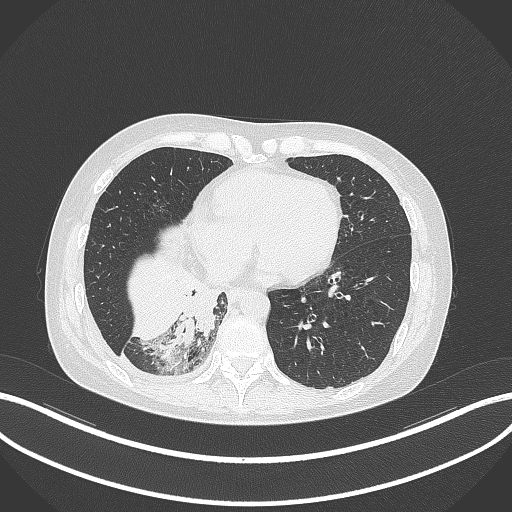
Chest CT, one axial slice; slice 97 of 329 in the series (ordered by position); 120 kVp; lung window (W 1500 / L -600 HU); 1 mm slice thickness; 512 × 512 image matrix, field of view 400 × 400 mm. Female patient, age 63 years. Case-level facts recorded for this patient, not image findings: clinical TNM (as recorded): T1c N0 M0.
Annotated regions visible in this slice (rectangle marked by the reading radiologist):
- lung tumour (recorded histology: adenocarcinoma): bounding box <165,277,221,340> (left, top, right, bottom; pixels)